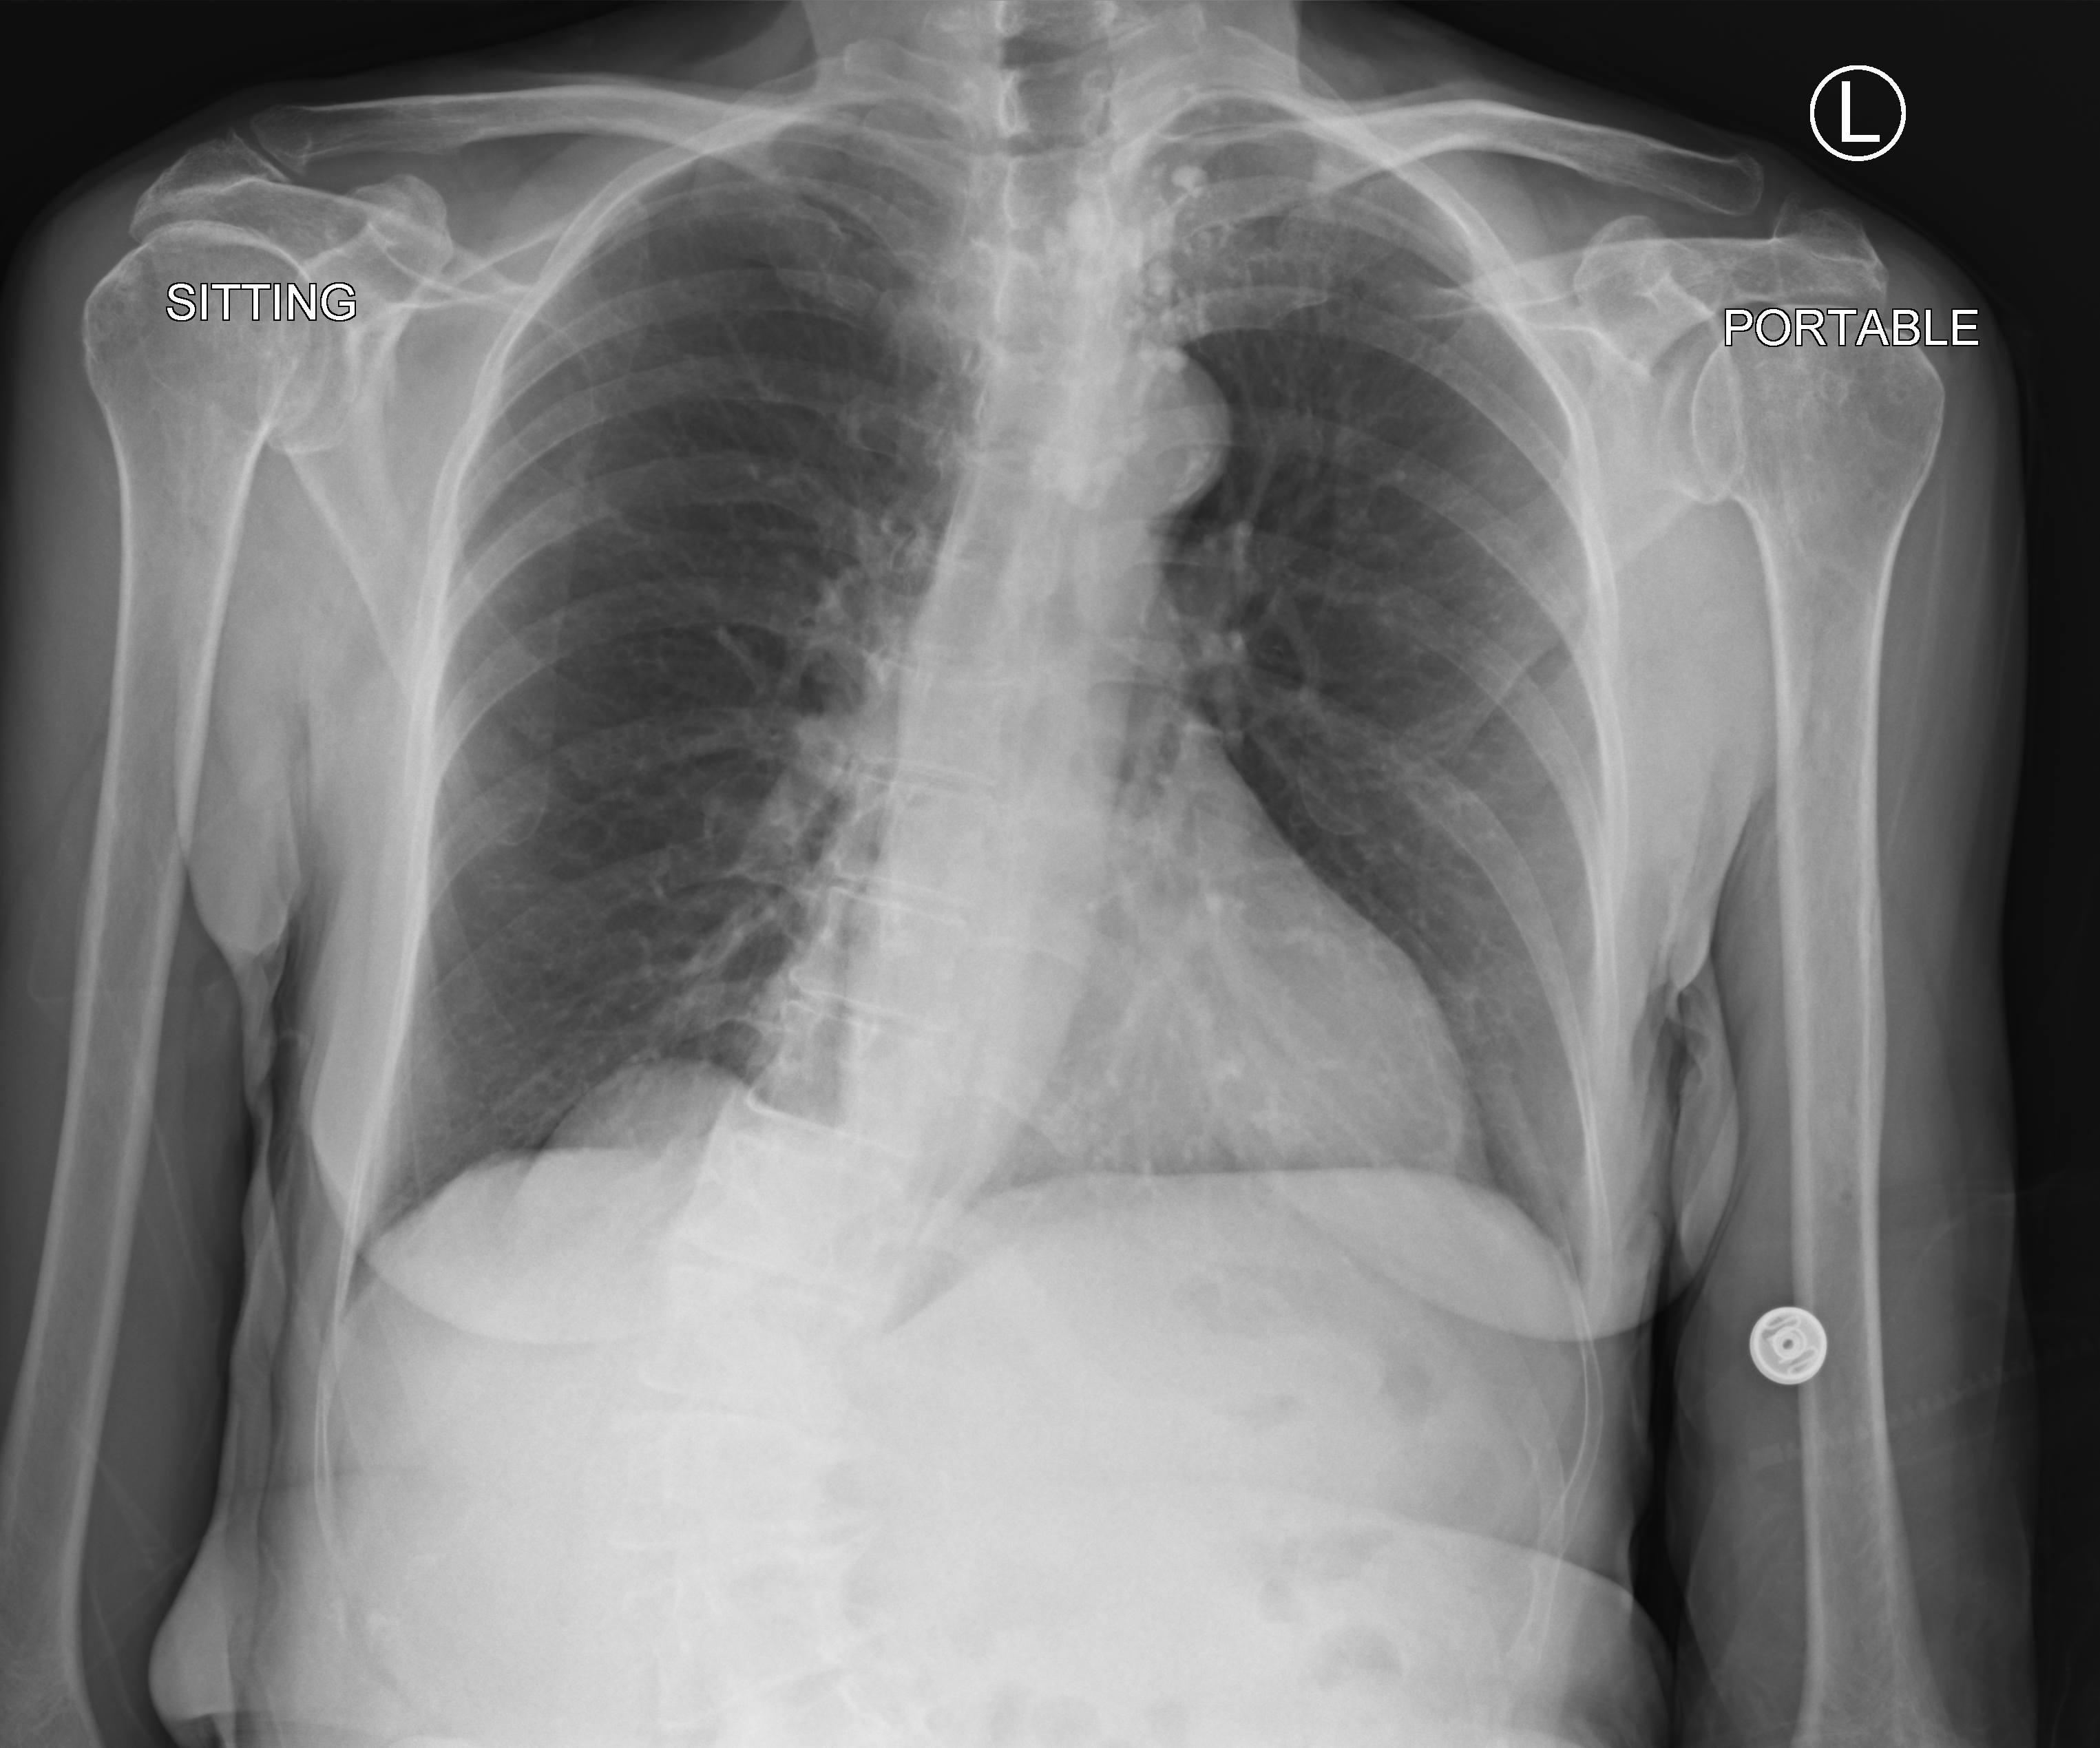
Portable chest radiograph; anteroposterior (AP) projection. Patient hospitalised with COVID-19; female, aged 60–74 years.
From the hospital-stay record, not from the radiograph (when in the stay this image was taken is not recorded): other chronic lung disease (admission record): no; diabetes (admission record): no; admitted to intensive care during this hospital stay: no.